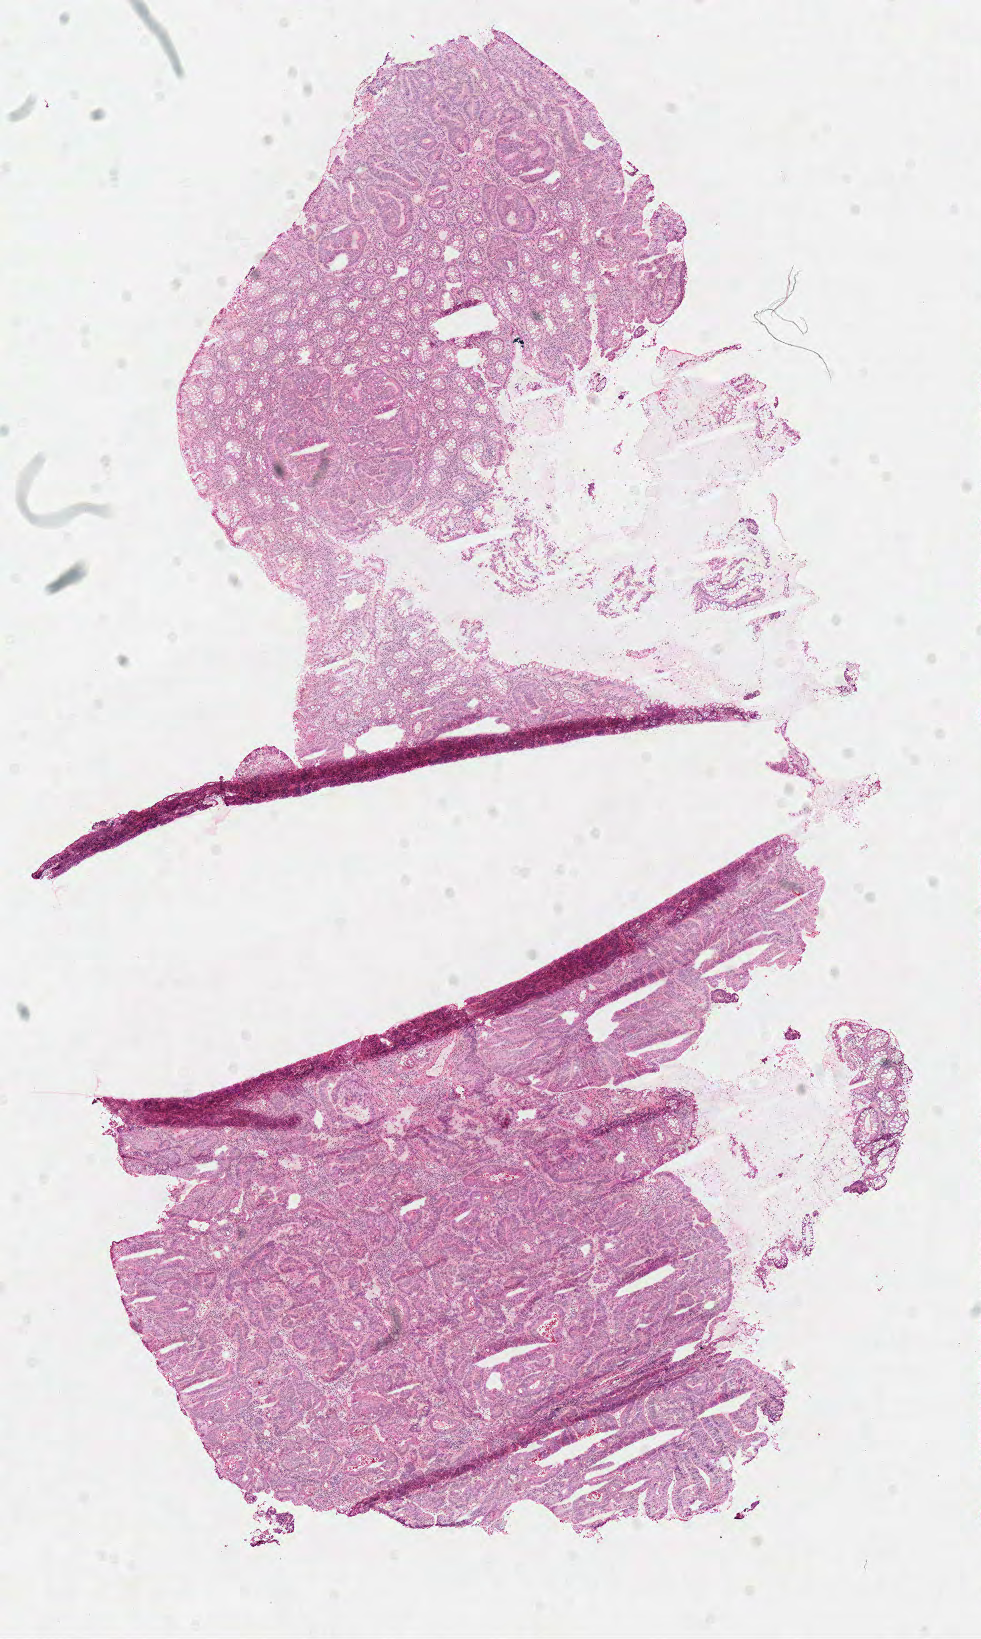
Digitized H&E-stained tissue section (whole slide) — low-resolution overview of the scanned area, about 7.7 x 12.9 mm, frozen section from the top of the tissue portion, rectum, primary tumour sample. Male, age 68 years at initial diagnosis. Pathologist review of this section (percent, as recorded): tumour cells 65%, tumour nuclei 75%, normal cells 20%, stromal cells 10%, necrosis 5%.
* AJCC pathologic stage: I (6th edition)
* lymph nodes positive (case pathology): 0 of 8 examined
* diagnosis: Adenocarcinoma, NOS
* TNM: T2 N0 M0